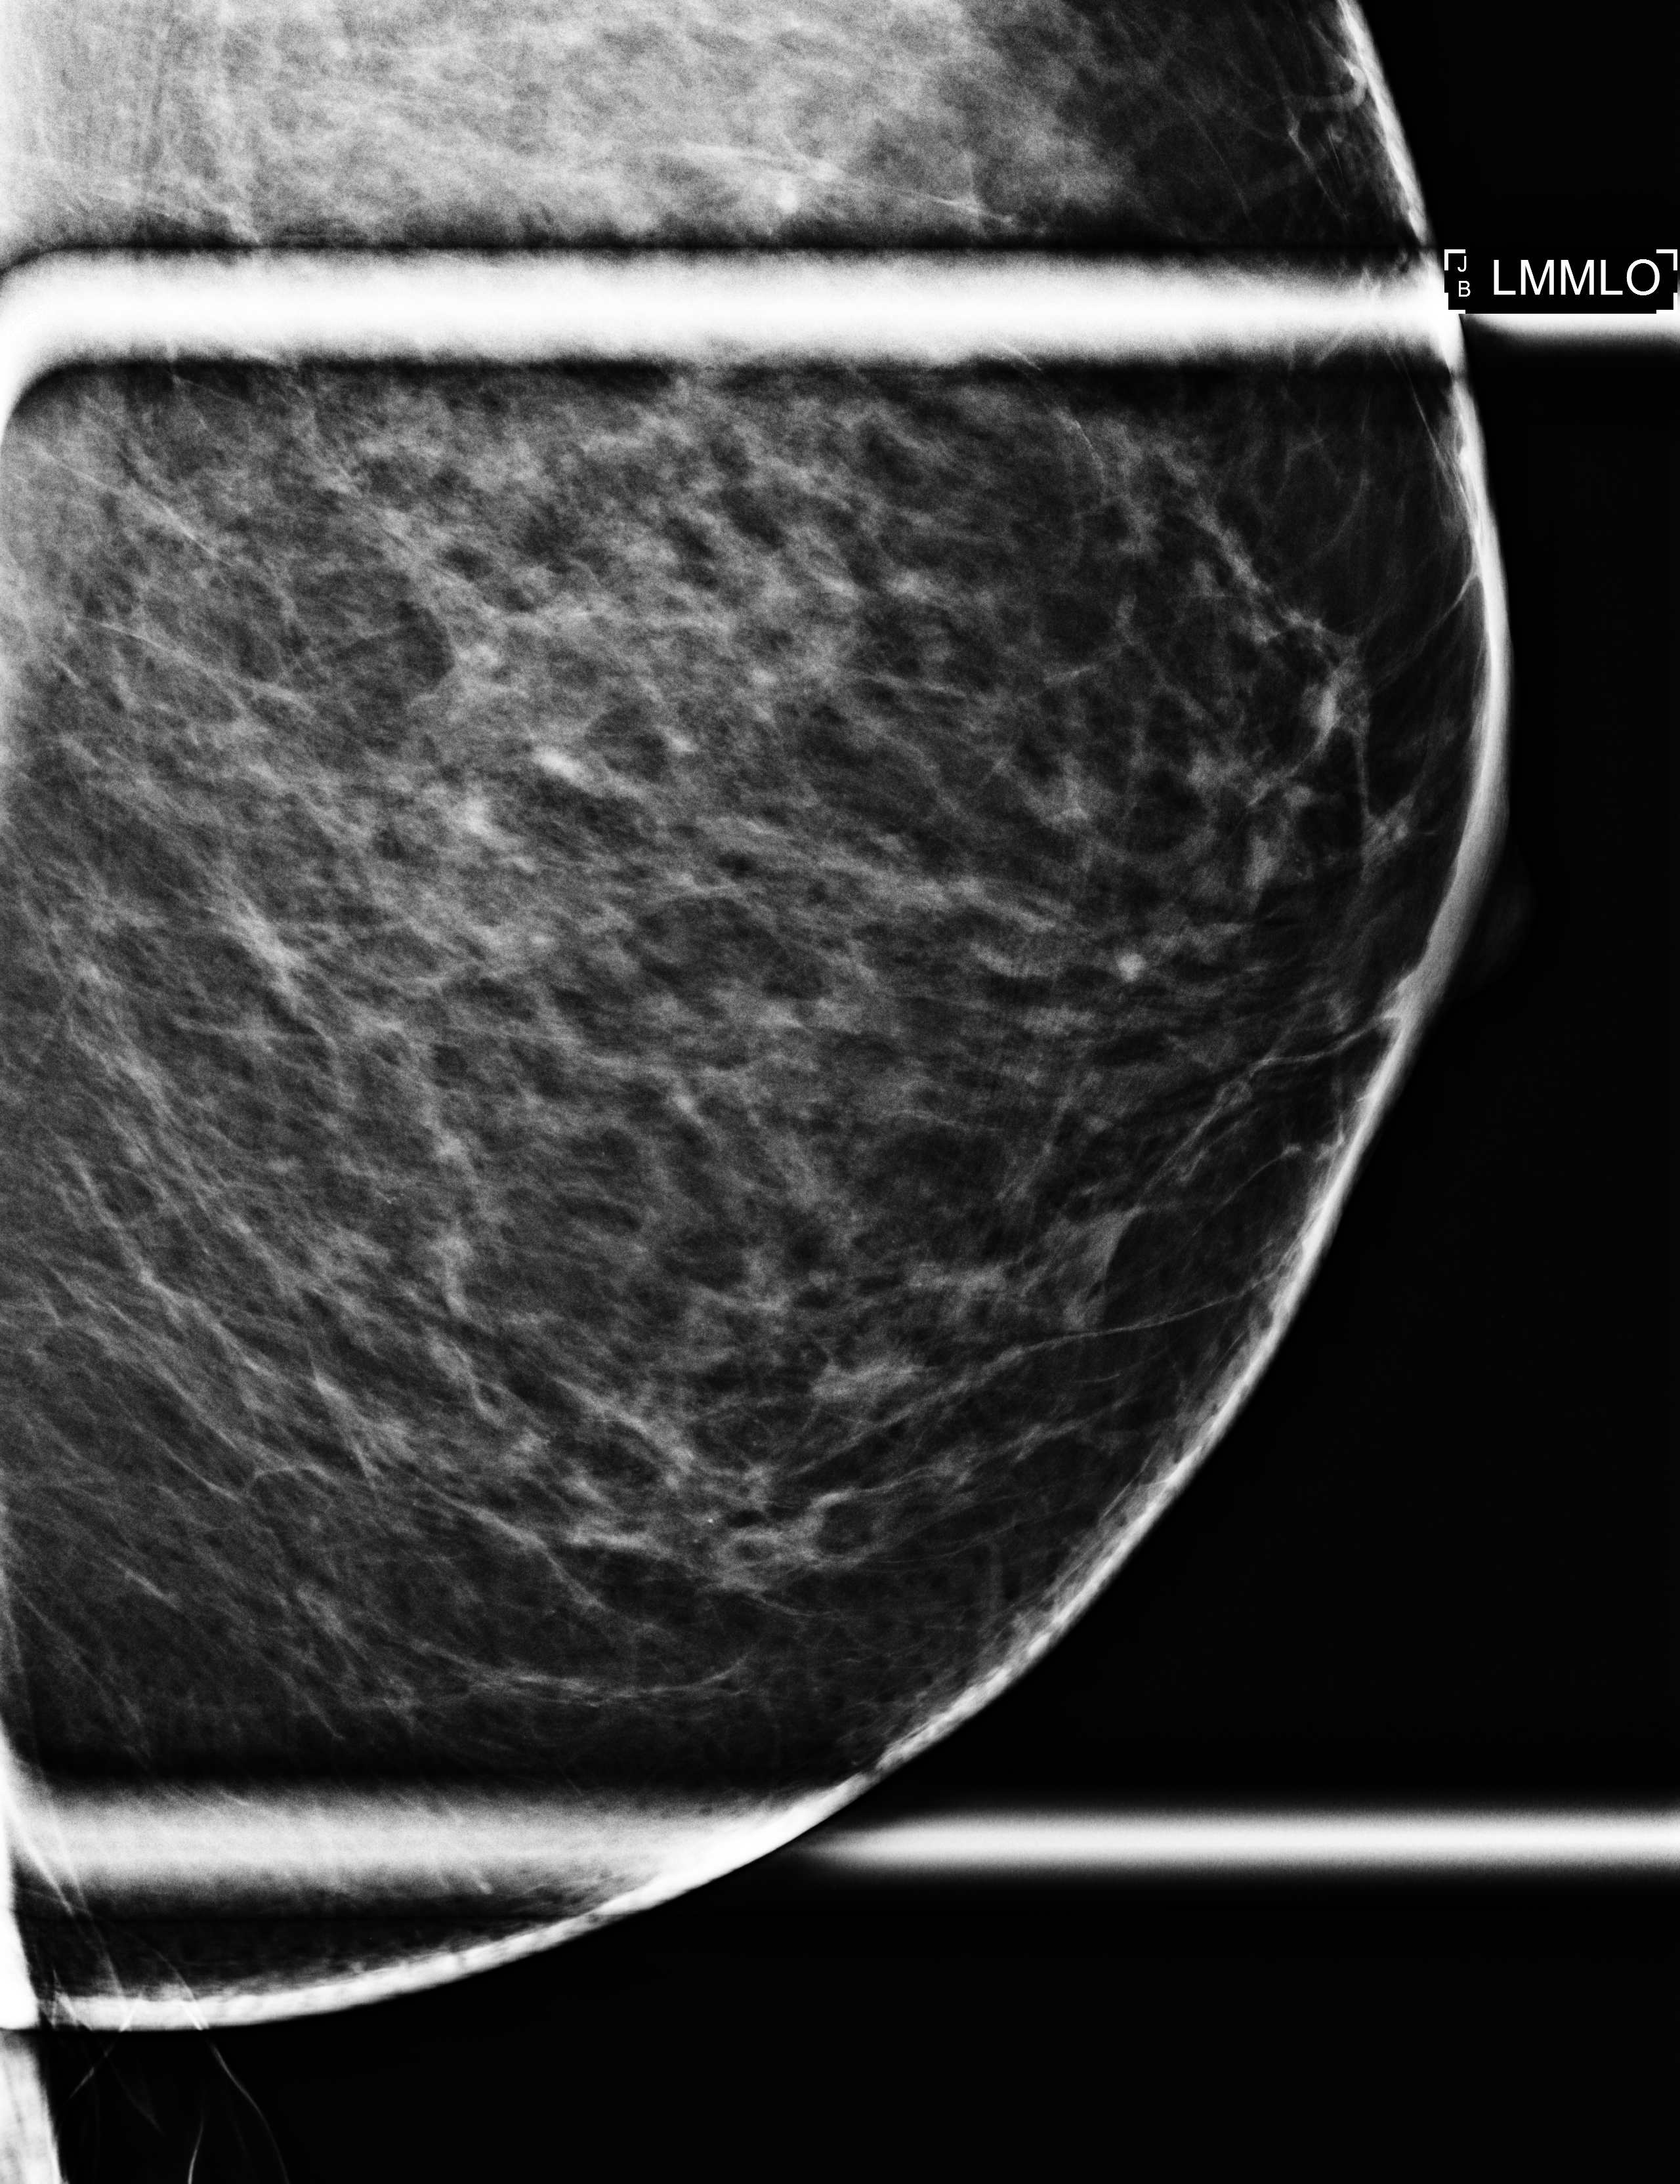
Digital mammogram (FFDM), left breast, mediolateral oblique (MLO) view (magnification), additional (diagnostic) view, compressed breast thickness 54 mm. Patient: female, 62 years.
BI-RADS breast density category at the screening exam (both breasts, scale 1–4): 2. Final BI-RADS category for the screening round (tomosynthesis exam, both breasts): category 2. Recall: recalled for additional imaging after this screen.